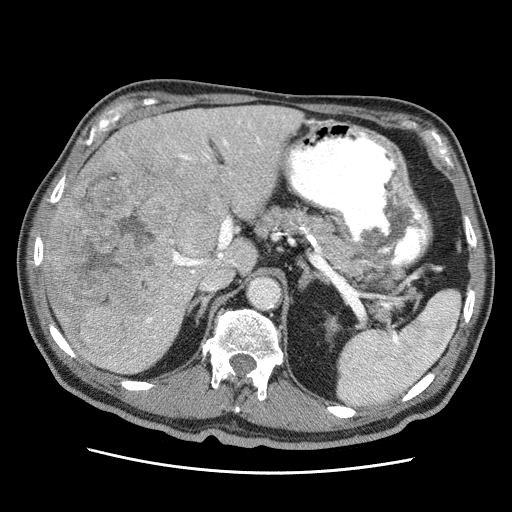
Contrast-enhanced abdominal CT (liver protocol), one axial slice. Slice 30 of 75 in the series (ordered by position). Soft-tissue window (W 400 / L 40 HU). 2.5 mm slice thickness. 512 × 512 image matrix, field of view 360 × 360 mm. From the clinical record (not read from this slice): diagnosis: hepatocellular carcinoma (patient treated with transarterial chemoembolisation; whether this scan precedes or follows treatment is not stated here); TNM stage (as recorded): Stage-IIIA; Child-Pugh class: A; tumour nodularity: multinodular; tumour size: 13.9 cm.
Structures marked on this image (semi-automatically segmented with operator editing):
- liver parenchyma outside the tumour (the mass and vessels are separate outlines, so this box may not span the whole liver): bounding box <44,104,302,374> (left, top, right, bottom; pixels)
- mass: <48,136,229,366>
- liver vessels: <115,116,274,365>